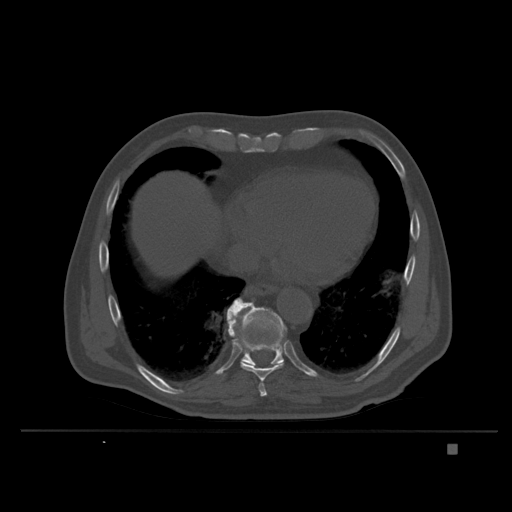
CT including the spine, one axial slice; bone window (W 1800 / L 400 HU); 512 × 512 image matrix. Patient: male, 73 years. From the clinical record (not read from this slice): primary cancer: skin.
Outlined on this slice (semi-automatically segmented with operator editing):
- T10 vertebra: bounding box (x1, y1, x2, y2) in pixels: (240, 302, 287, 366)
- T9 vertebra: (227, 298, 284, 397)